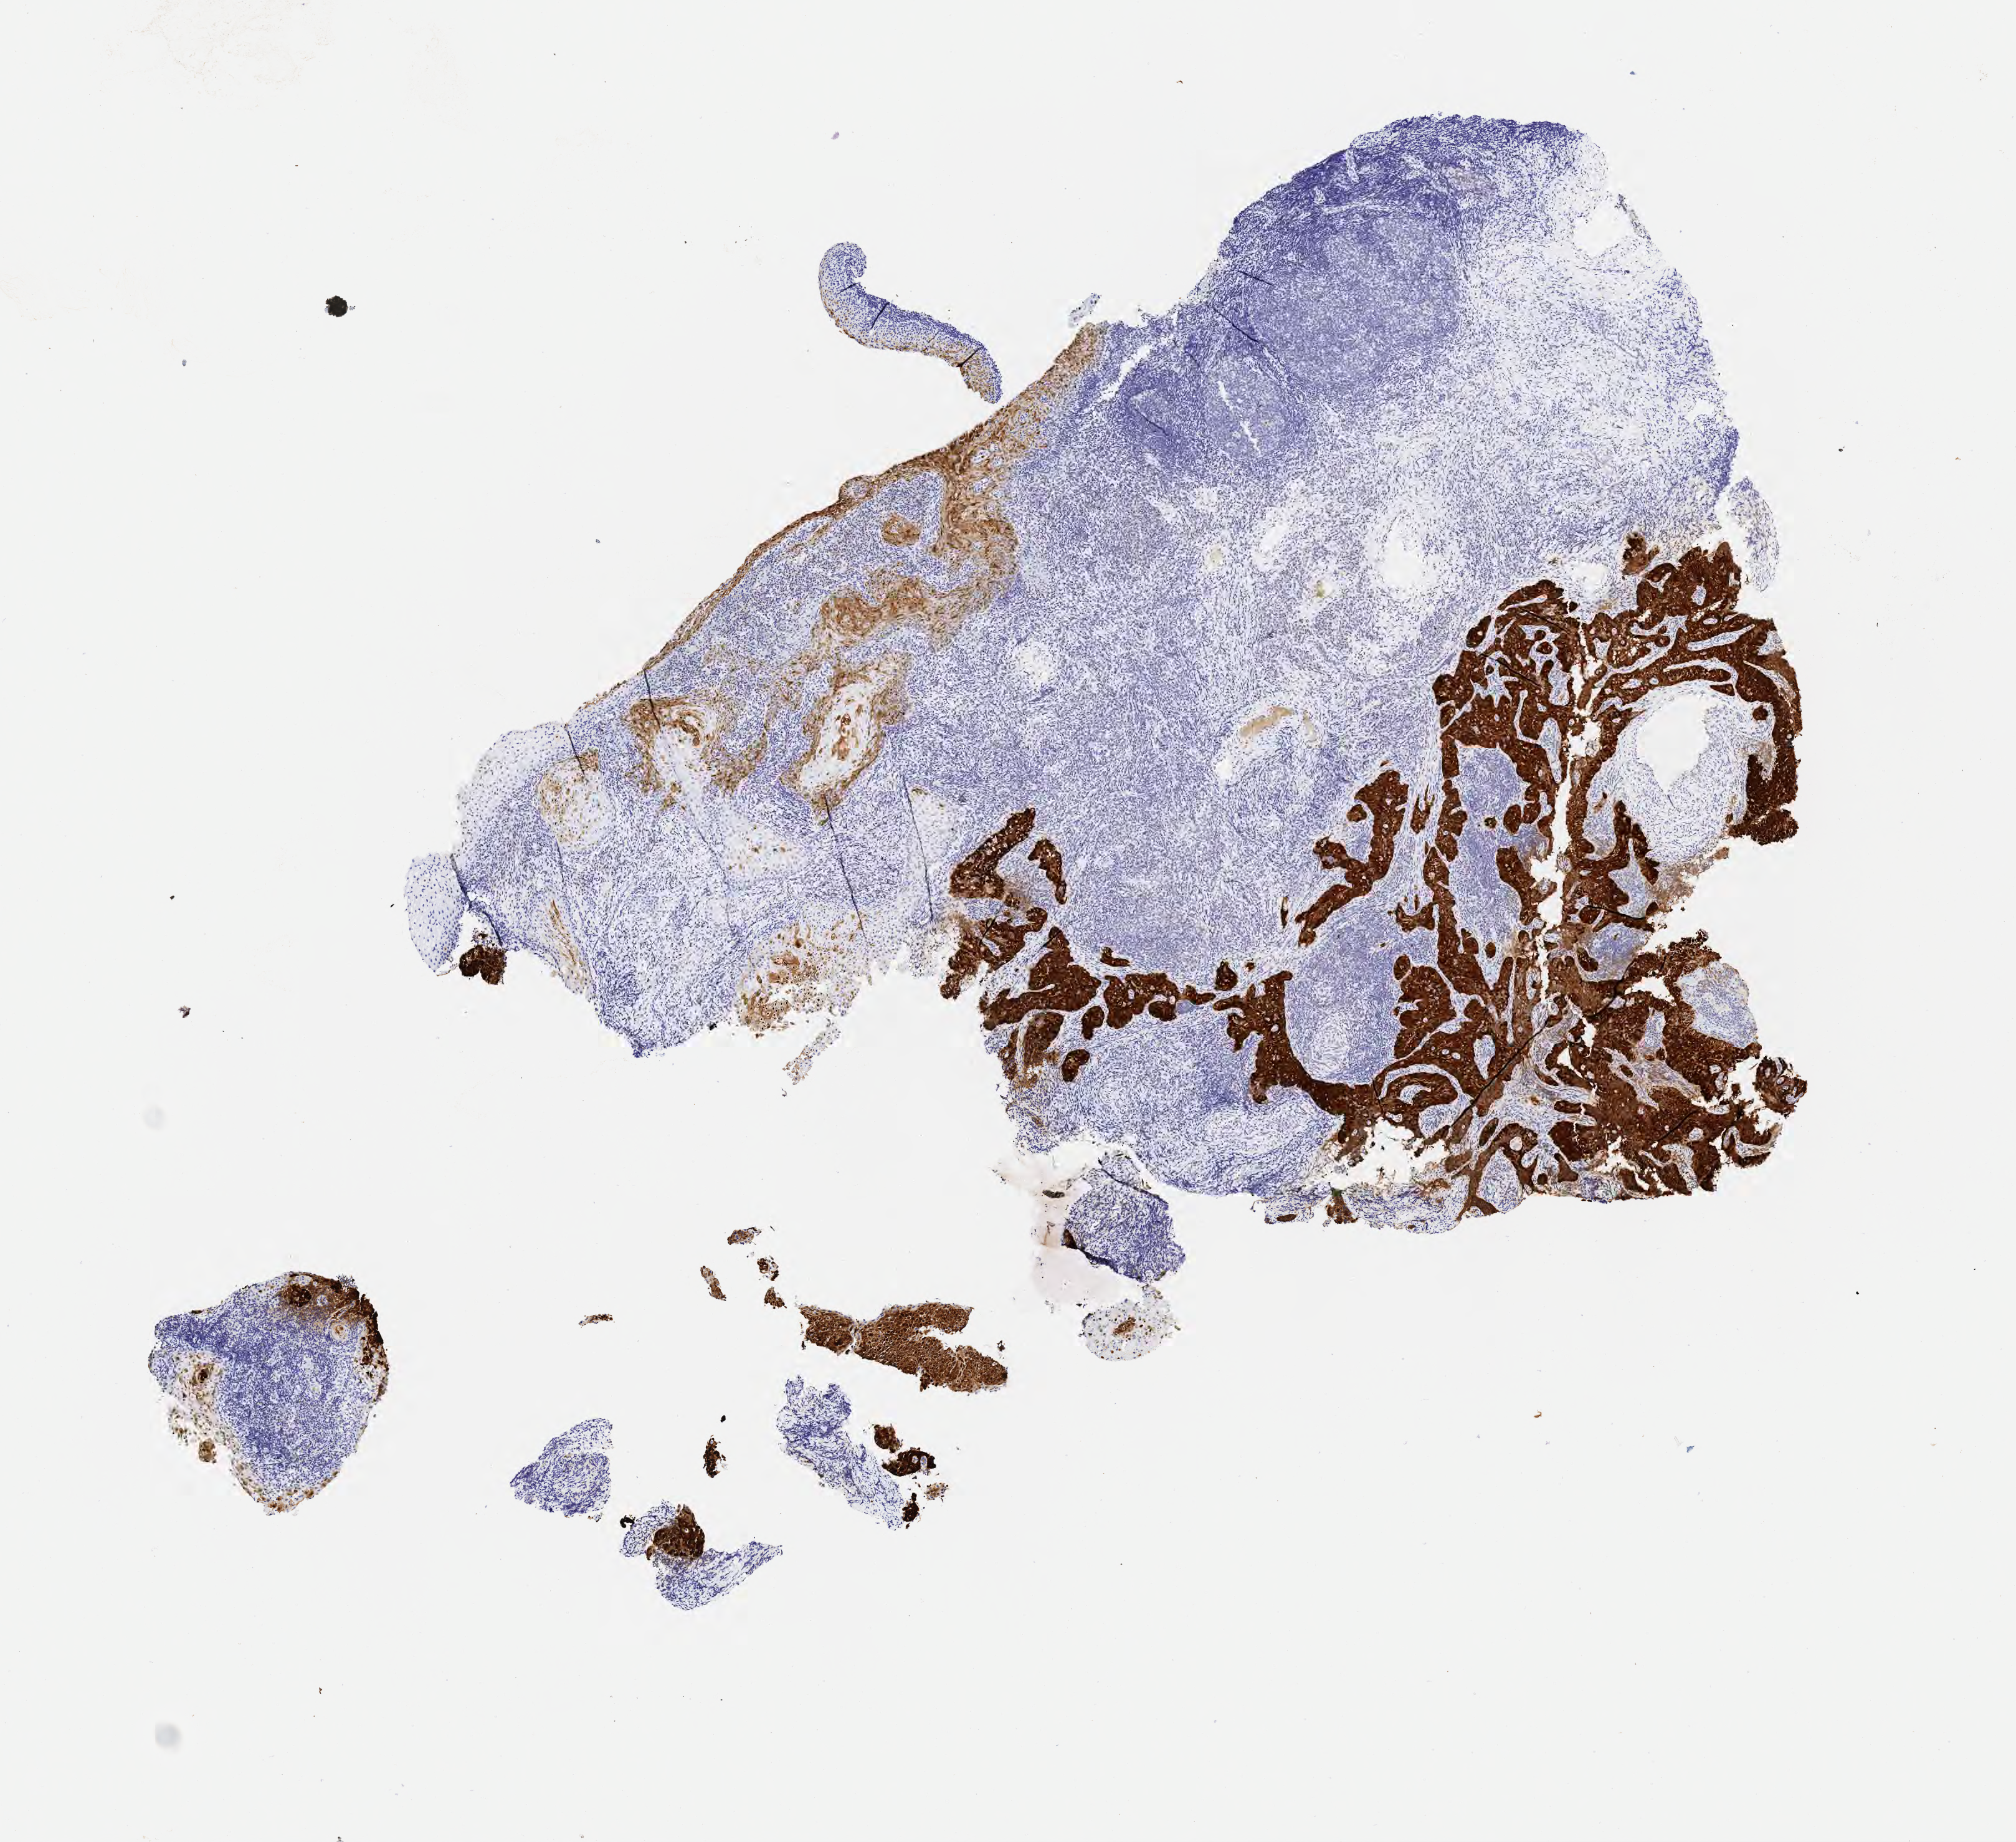
IHC for p16 (p16INK4a), whole-slide image, shown as a low-resolution overview of the whole scanned area (about 6.5 x 6.0 mm), specimen: tumor tissue, site: cervix. Patient: female, aged 36.
- histologic diagnosis: Squamous cell carcinoma, large cell, nonkeratinizing, NOS